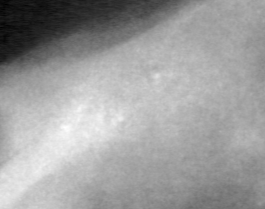
Cropped region of a digitized screen-film mammogram centred on a radiologist-marked abnormality; left breast; CC view.
- Marked abnormality: calcifications, morphology pleomorphic, distribution clustered; BI-RADS assessment category 4; subtlety rating 1 on a 1 (subtle) to 5 (obvious) scale; pathology (as recorded): benign.